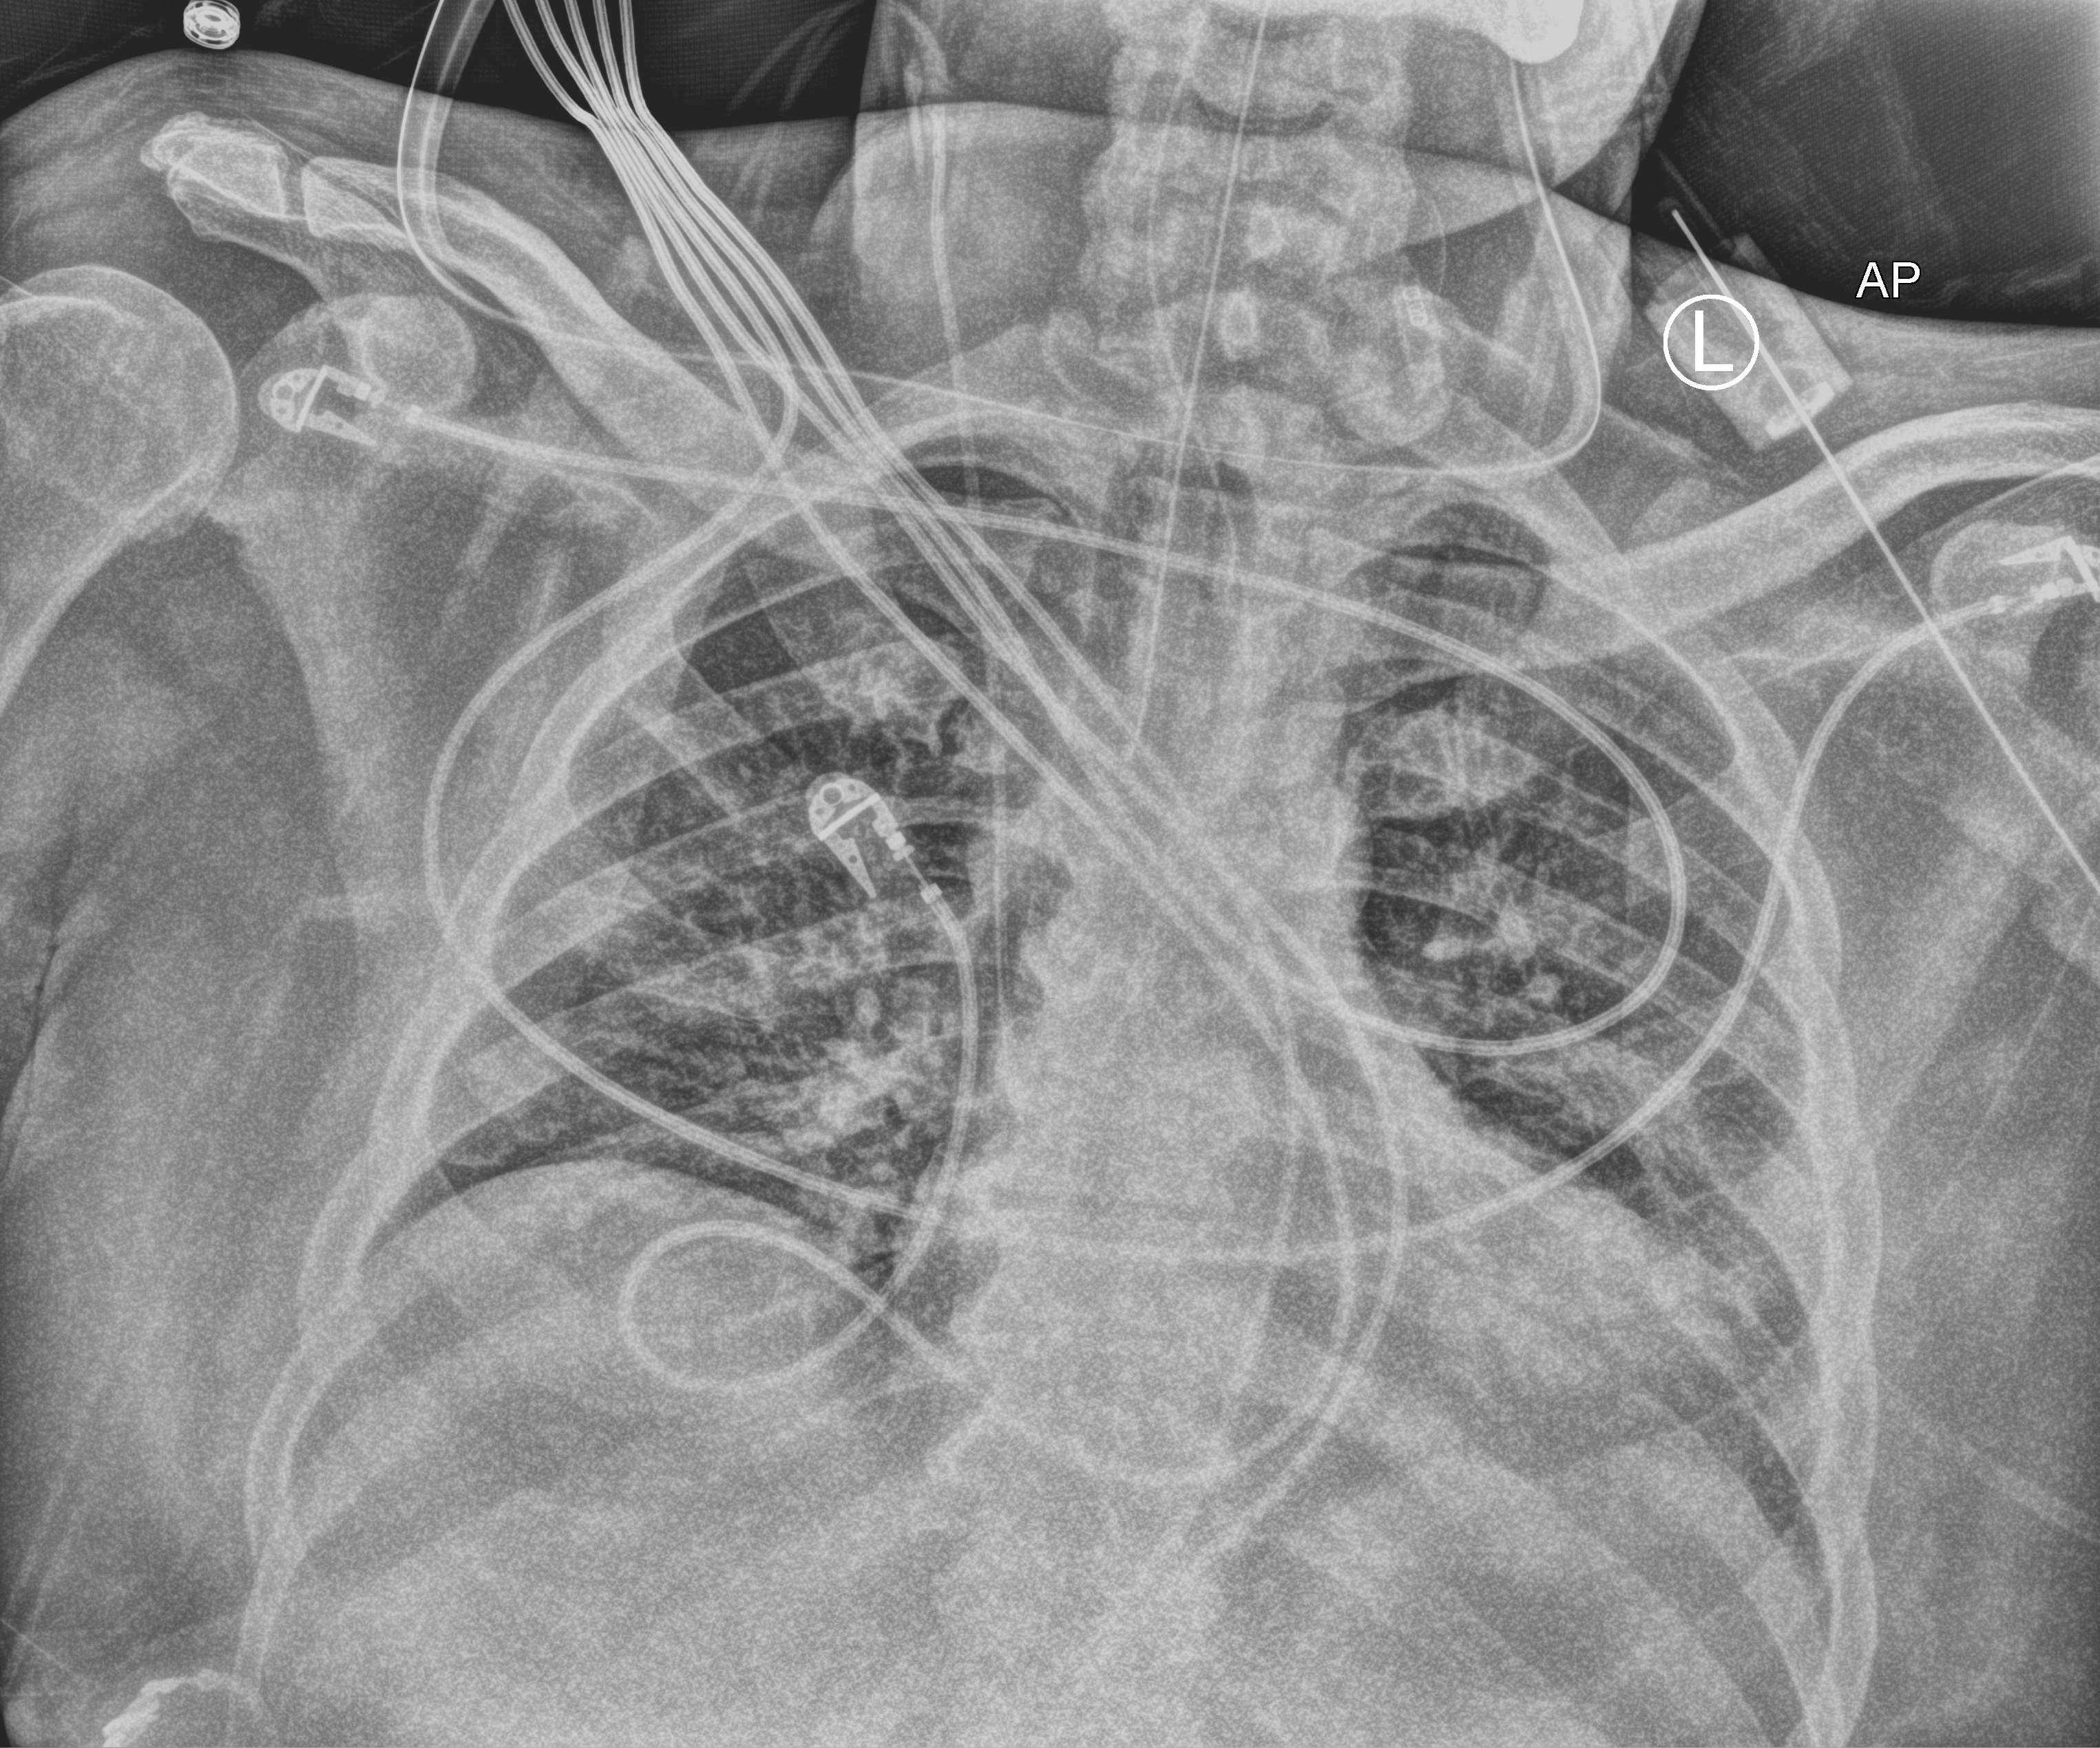
Bedside chest radiograph (computed radiography). Patient hospitalised with COVID-19; male, aged 18–59 years.
From the hospital-stay record, not from the radiograph (when in the stay this image was taken is not recorded):
- admitted to intensive care during this hospital stay: yes
- chronic kidney disease (admission record): no
- diabetes (admission record): no